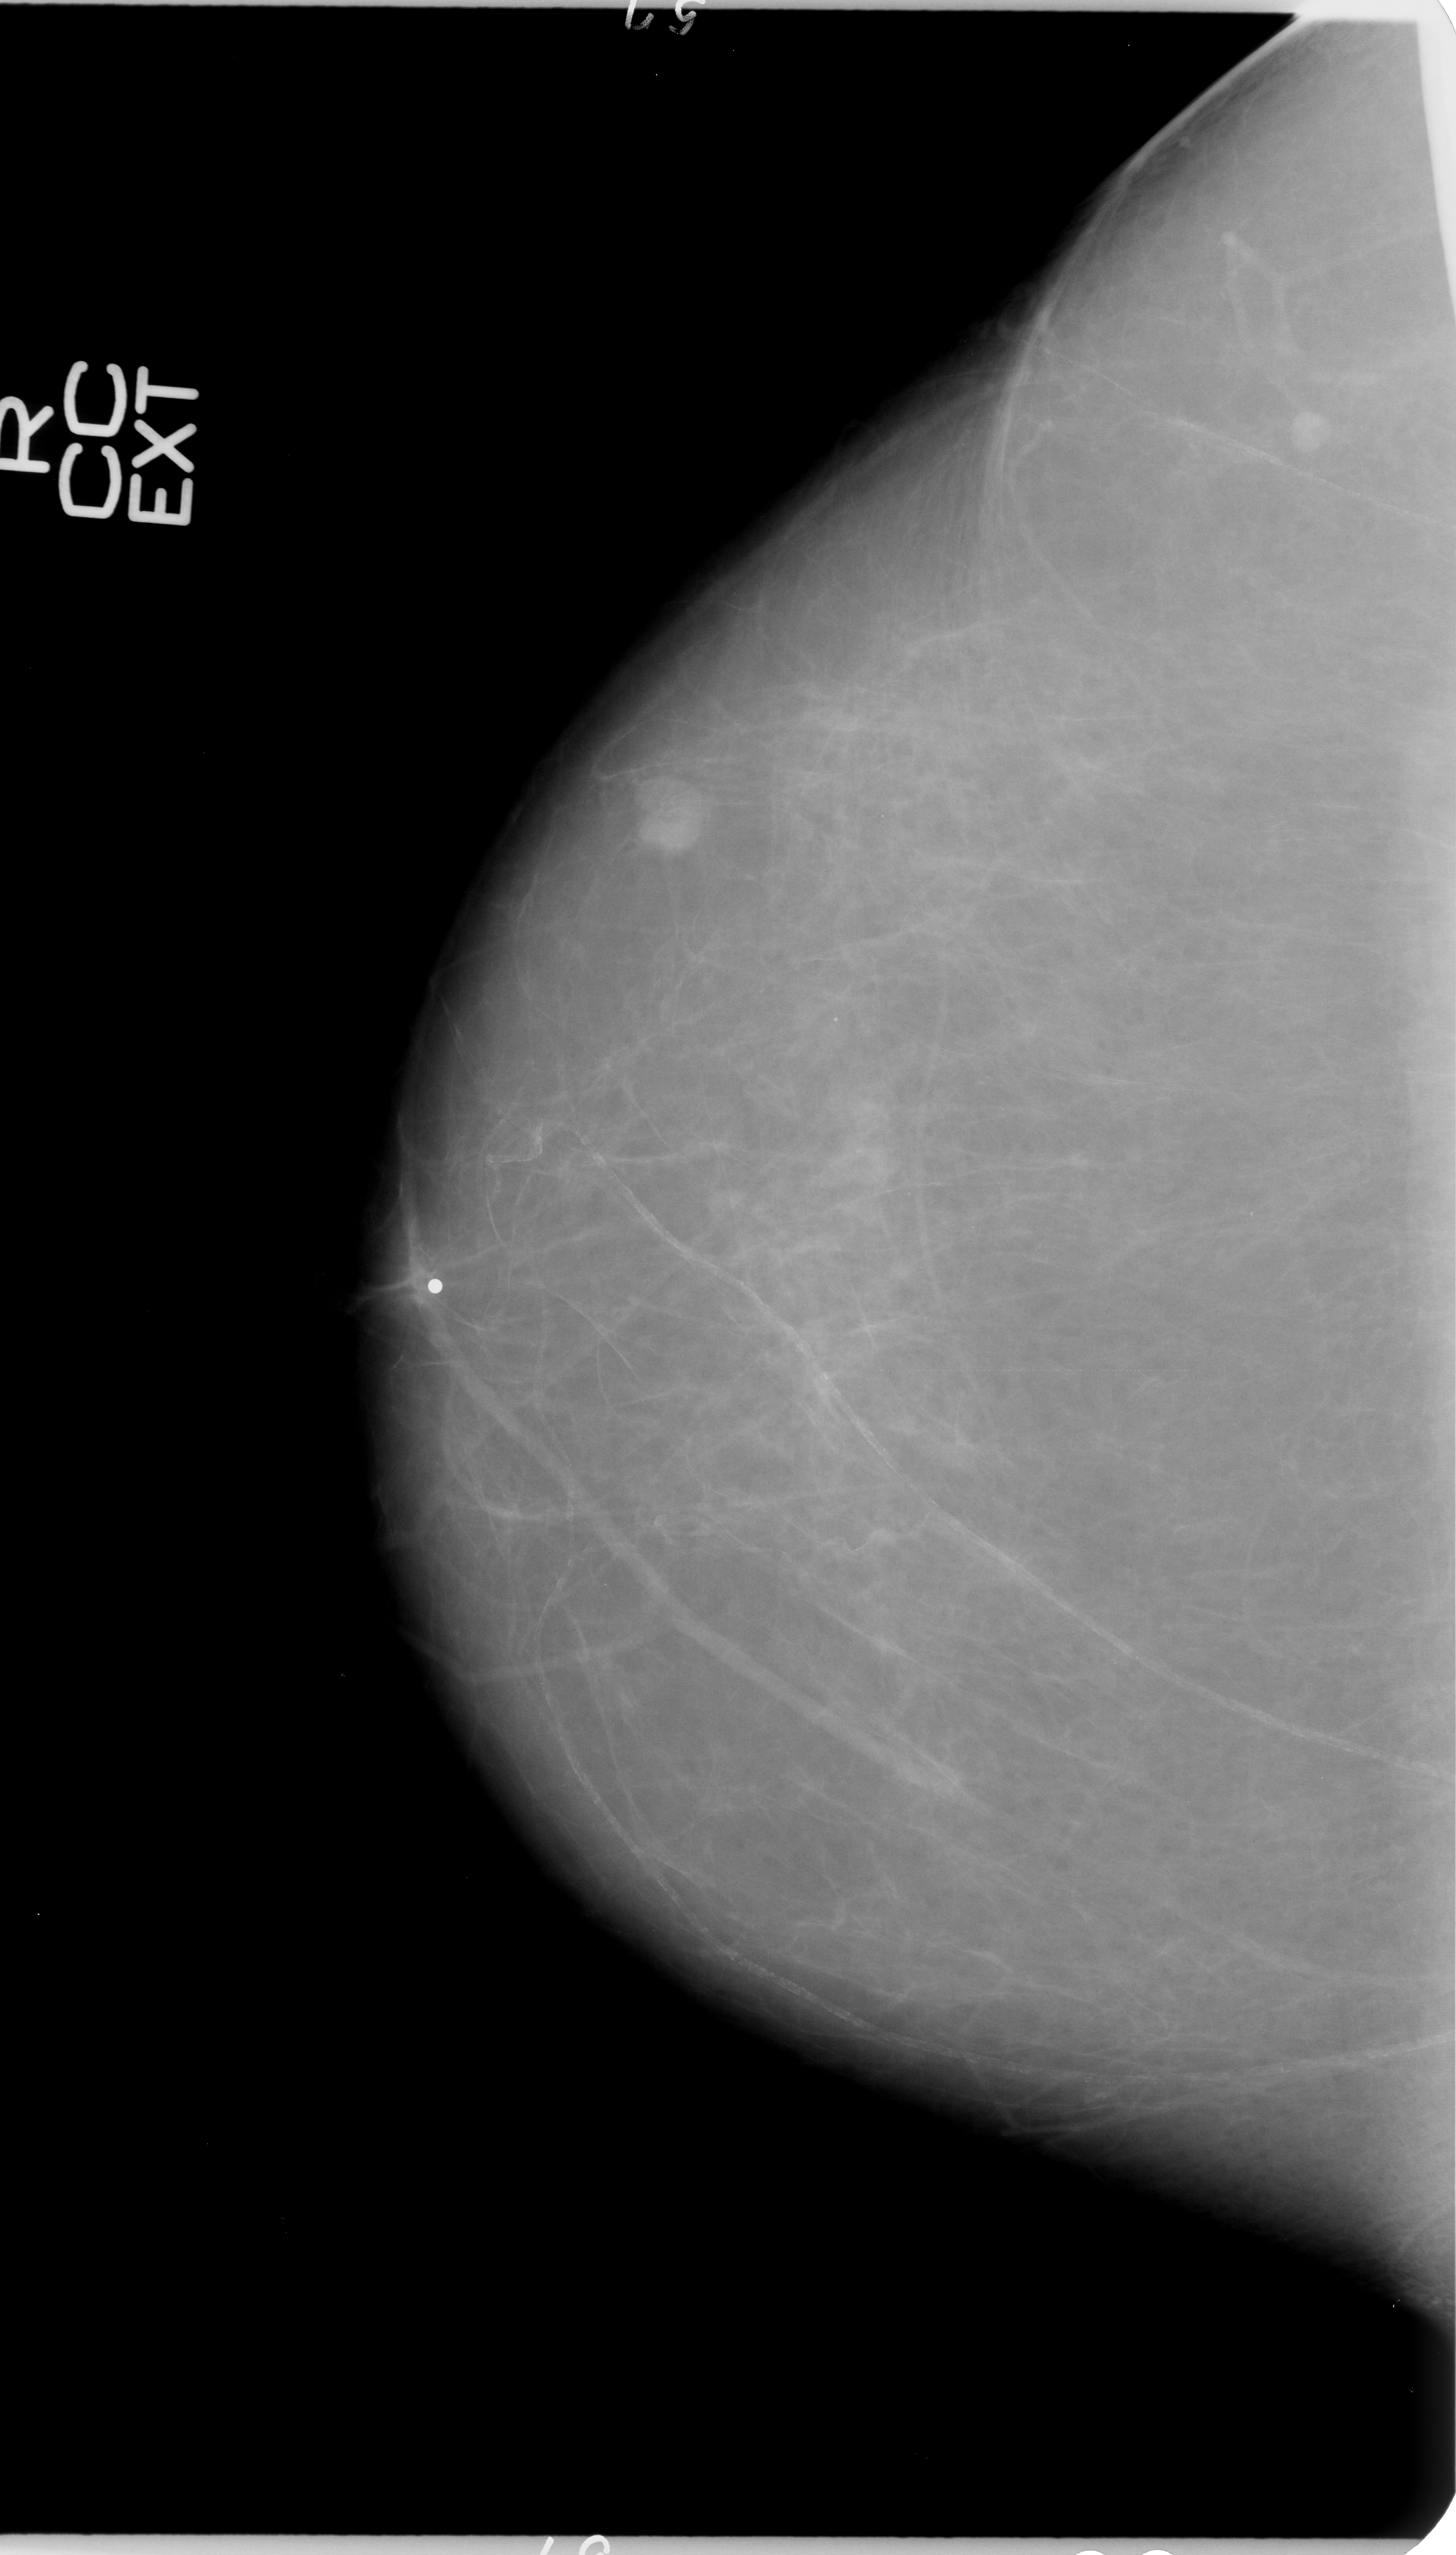
Scanned film-screen mammogram, right breast, craniocaudal (CC) view, breast composition: almost entirely fatty (BI-RADS density category 1 of 4).
Marked findings (only marked abnormalities are described; nothing is implied about the rest of the image): mass, shape irregular, margins ill defined; BI-RADS assessment category 1; pathology (as recorded): malignant.